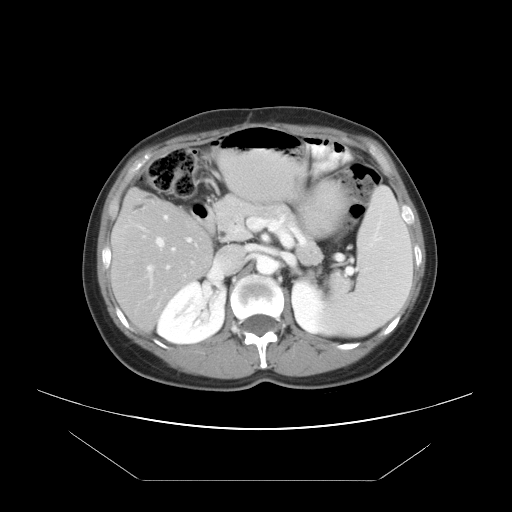
Contrast-enhanced abdominal CT, one axial slice; slice 23 of 45 in the series (ordered by position); reconstruction kernel STANDARD; 120 kVp; intravenous contrast given; soft-tissue window (W 400 / L 40 HU); 5 mm slice thickness; 512 × 512 image matrix, field of view 405 × 405 mm. Female patient, age 52 years. Case-level facts recorded for this patient, not image findings: diagnosis: colorectal cancer liver metastases, imaged before liver resection; multiple liver metastases: yes; largest metastasis: 2.5 cm; disease in both lobes: no.
Structures marked on this image (outlined manually by an expert reader):
- hepatic veins: box from (x=147, y=237) to (x=170, y=270) px
- liver: (x=112, y=191)–(x=209, y=330)
- planned liver remnant (the part of the liver to remain after resection): (x=112, y=191)–(x=209, y=330)
- portal vein (with intrahepatic branches): (x=143, y=215)–(x=193, y=252)